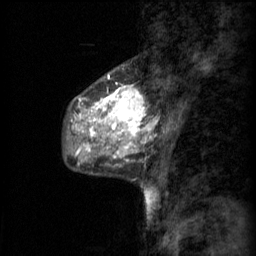
Breast MRI (dynamic contrast-enhanced), one sagittal slice. Position 22 of 60 along the scan axis. 3 images stored at this slice position (order not interpretable as contrast timing). 1.5 T. TE 4.2 ms, TR 11 ms. 2 mm slice thickness. 256 × 256 image matrix, field of view 200 × 200 mm. Female patient, age 48 years.
Outlined on this slice (semi-automatic segmentation, software-assisted and operator-edited):
- analysis volume of interest (the breast-tissue region the enhancement analysis was run in; not a lesion): bounding box (x1, y1, x2, y2) in pixels: (69, 74, 152, 147)
- tumour enhancement mask (voxels above the 70 % enhancement threshold inside the analysis volume of interest): (76, 74, 144, 147)